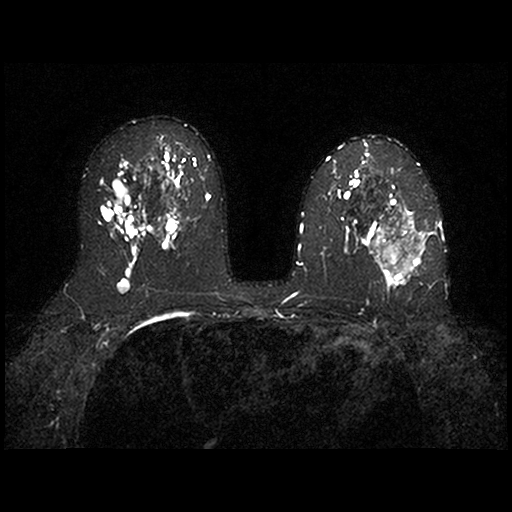
MRI of the breasts; 2 images, each one mid-volume slice chosen by position.
Image 1: fluid-sensitive (T2/STIR) axial slice, slice 43 of 84, 2 mm slice thickness.
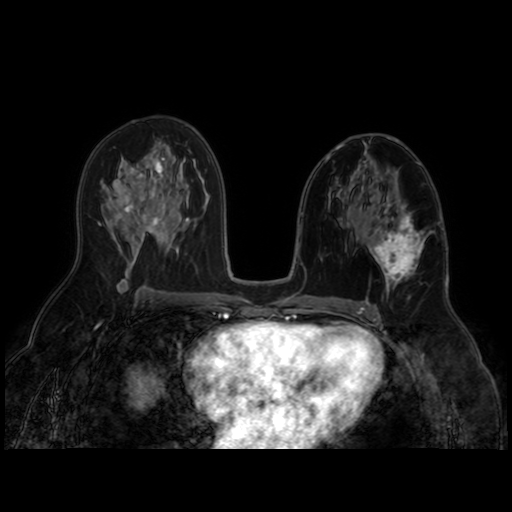
Image 2: post-contrast dynamic axial slice, slice 43 of 84, dynamic phase 5 of 8.
Patient-level pathology facts (from the clinical record, not from the images): pathology diagnosis: invasive ductal CA (left breast); receptor status (as recorded): ER neg, PR neg, HER2 neg; Ki-67 (as recorded): high prolif; pathology report notes: mastectomy.